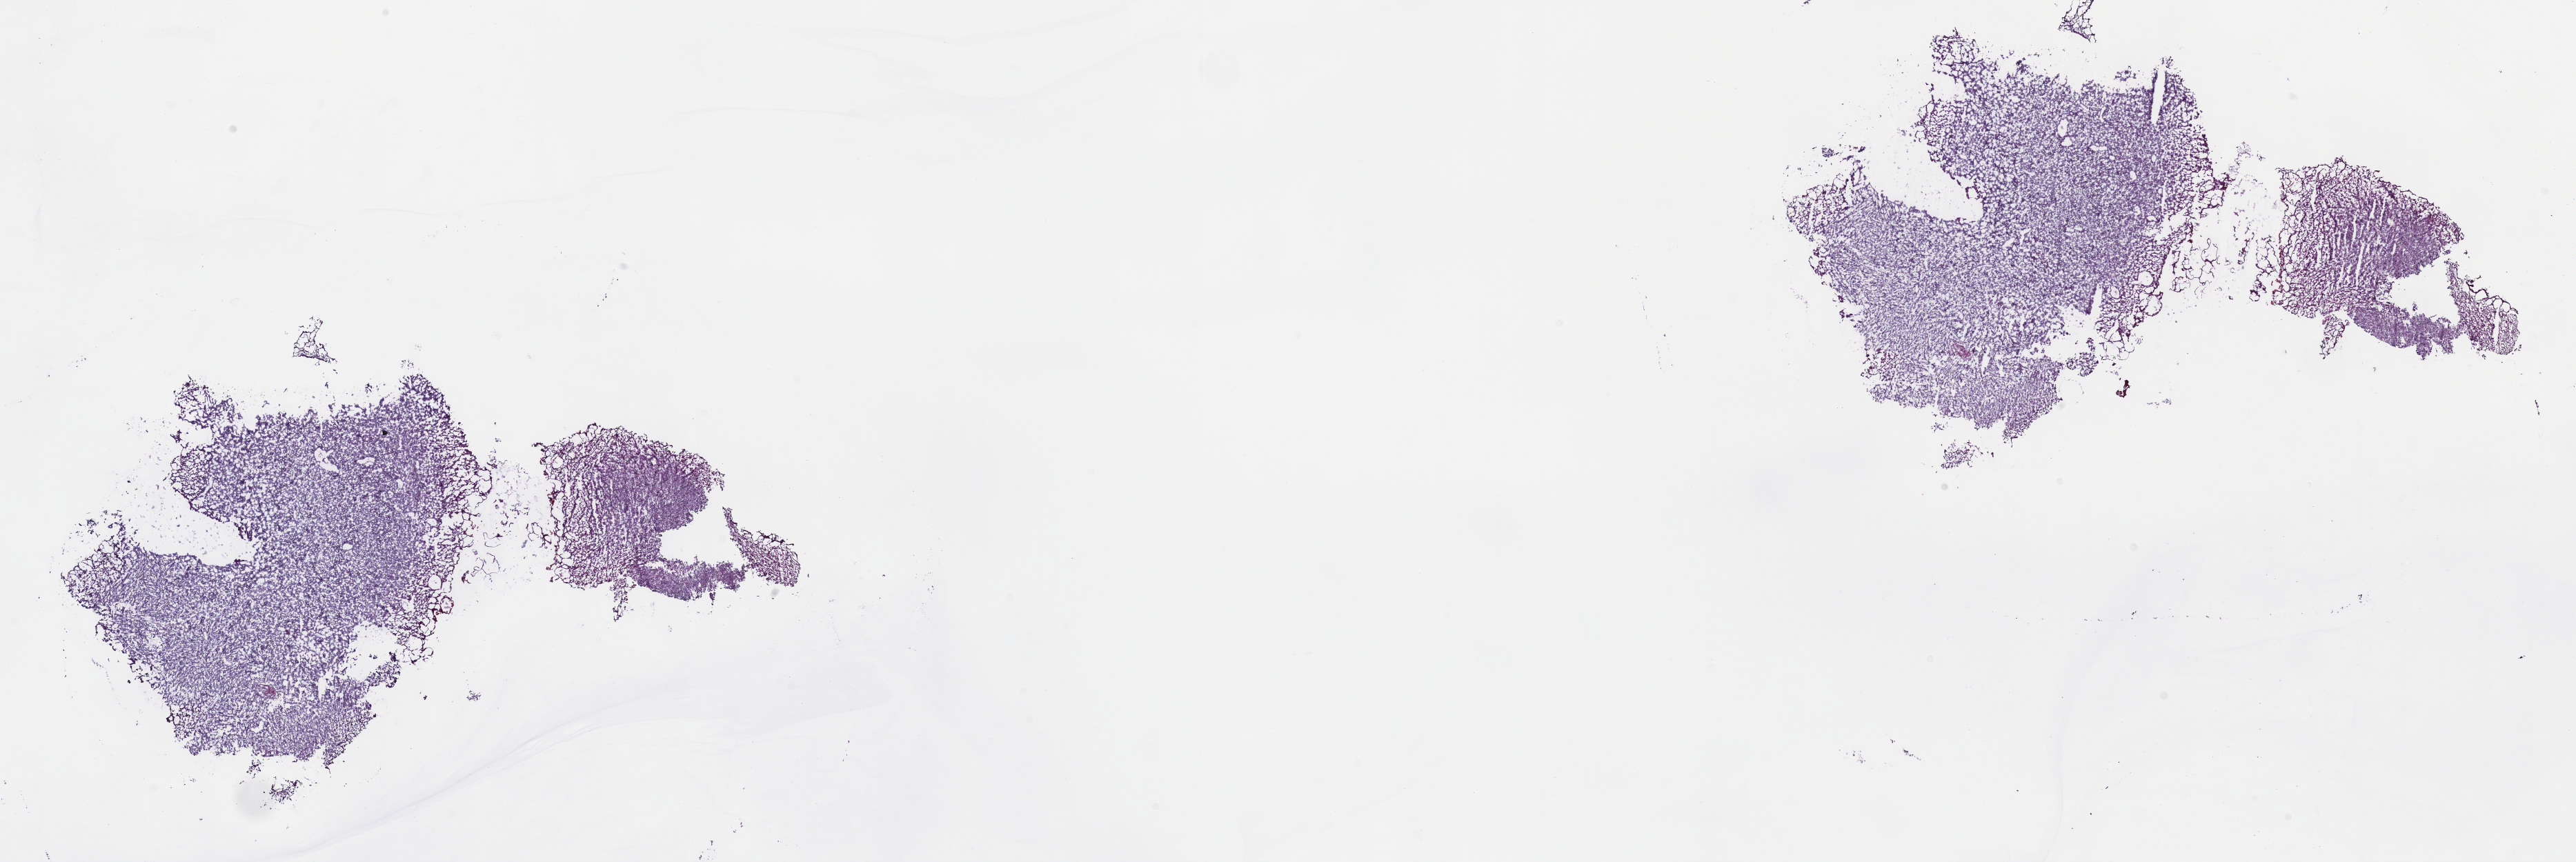
Digitized H&E tissue section (whole slide) — shown as a low-resolution overview of the whole scanned area (about 30.2 x 10.1 mm, acquisition: 40x scan). Frozen section from the top of the tissue portion. Primary tumour sample from the bladder. Male patient; age at initial diagnosis 66 years. Histologic grade: high grade. Slide review estimates, as recorded: tumour cells 100%, tumour nuclei 80%, normal cells 0%, stromal cells 0%, necrosis 0%. Infiltration values recorded for this section: lymphocyte infiltration 2%, monocyte infiltration 0%, neutrophil infiltration 0%.
• lymph nodes positive (case pathology): 1 of 45 examined
• AJCC pathologic stage: IV (6th edition)
• pathologic diagnosis: Transitional cell carcinoma